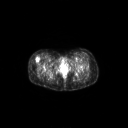
FDG PET of an extremity soft-tissue mass (from a PET/CT study), one axial slice; position 52 of 267 along the scan axis; 3.27 mm slice thickness; 128 × 128 image matrix. Patient: female, 34 years. Case-level facts recorded for this patient, not image findings: histological type: synovial sarcoma; grade: intermediate; site of the primary tumour: right thigh.
Structures marked on this image (expert contour drawn on MRI and transferred to this co-registered scan by the dataset authors):
- gross tumour volume including surrounding oedema: box from (x=34, y=57) to (x=39, y=62) px
- gross tumour volume (mass): (x=34, y=57)–(x=39, y=62)